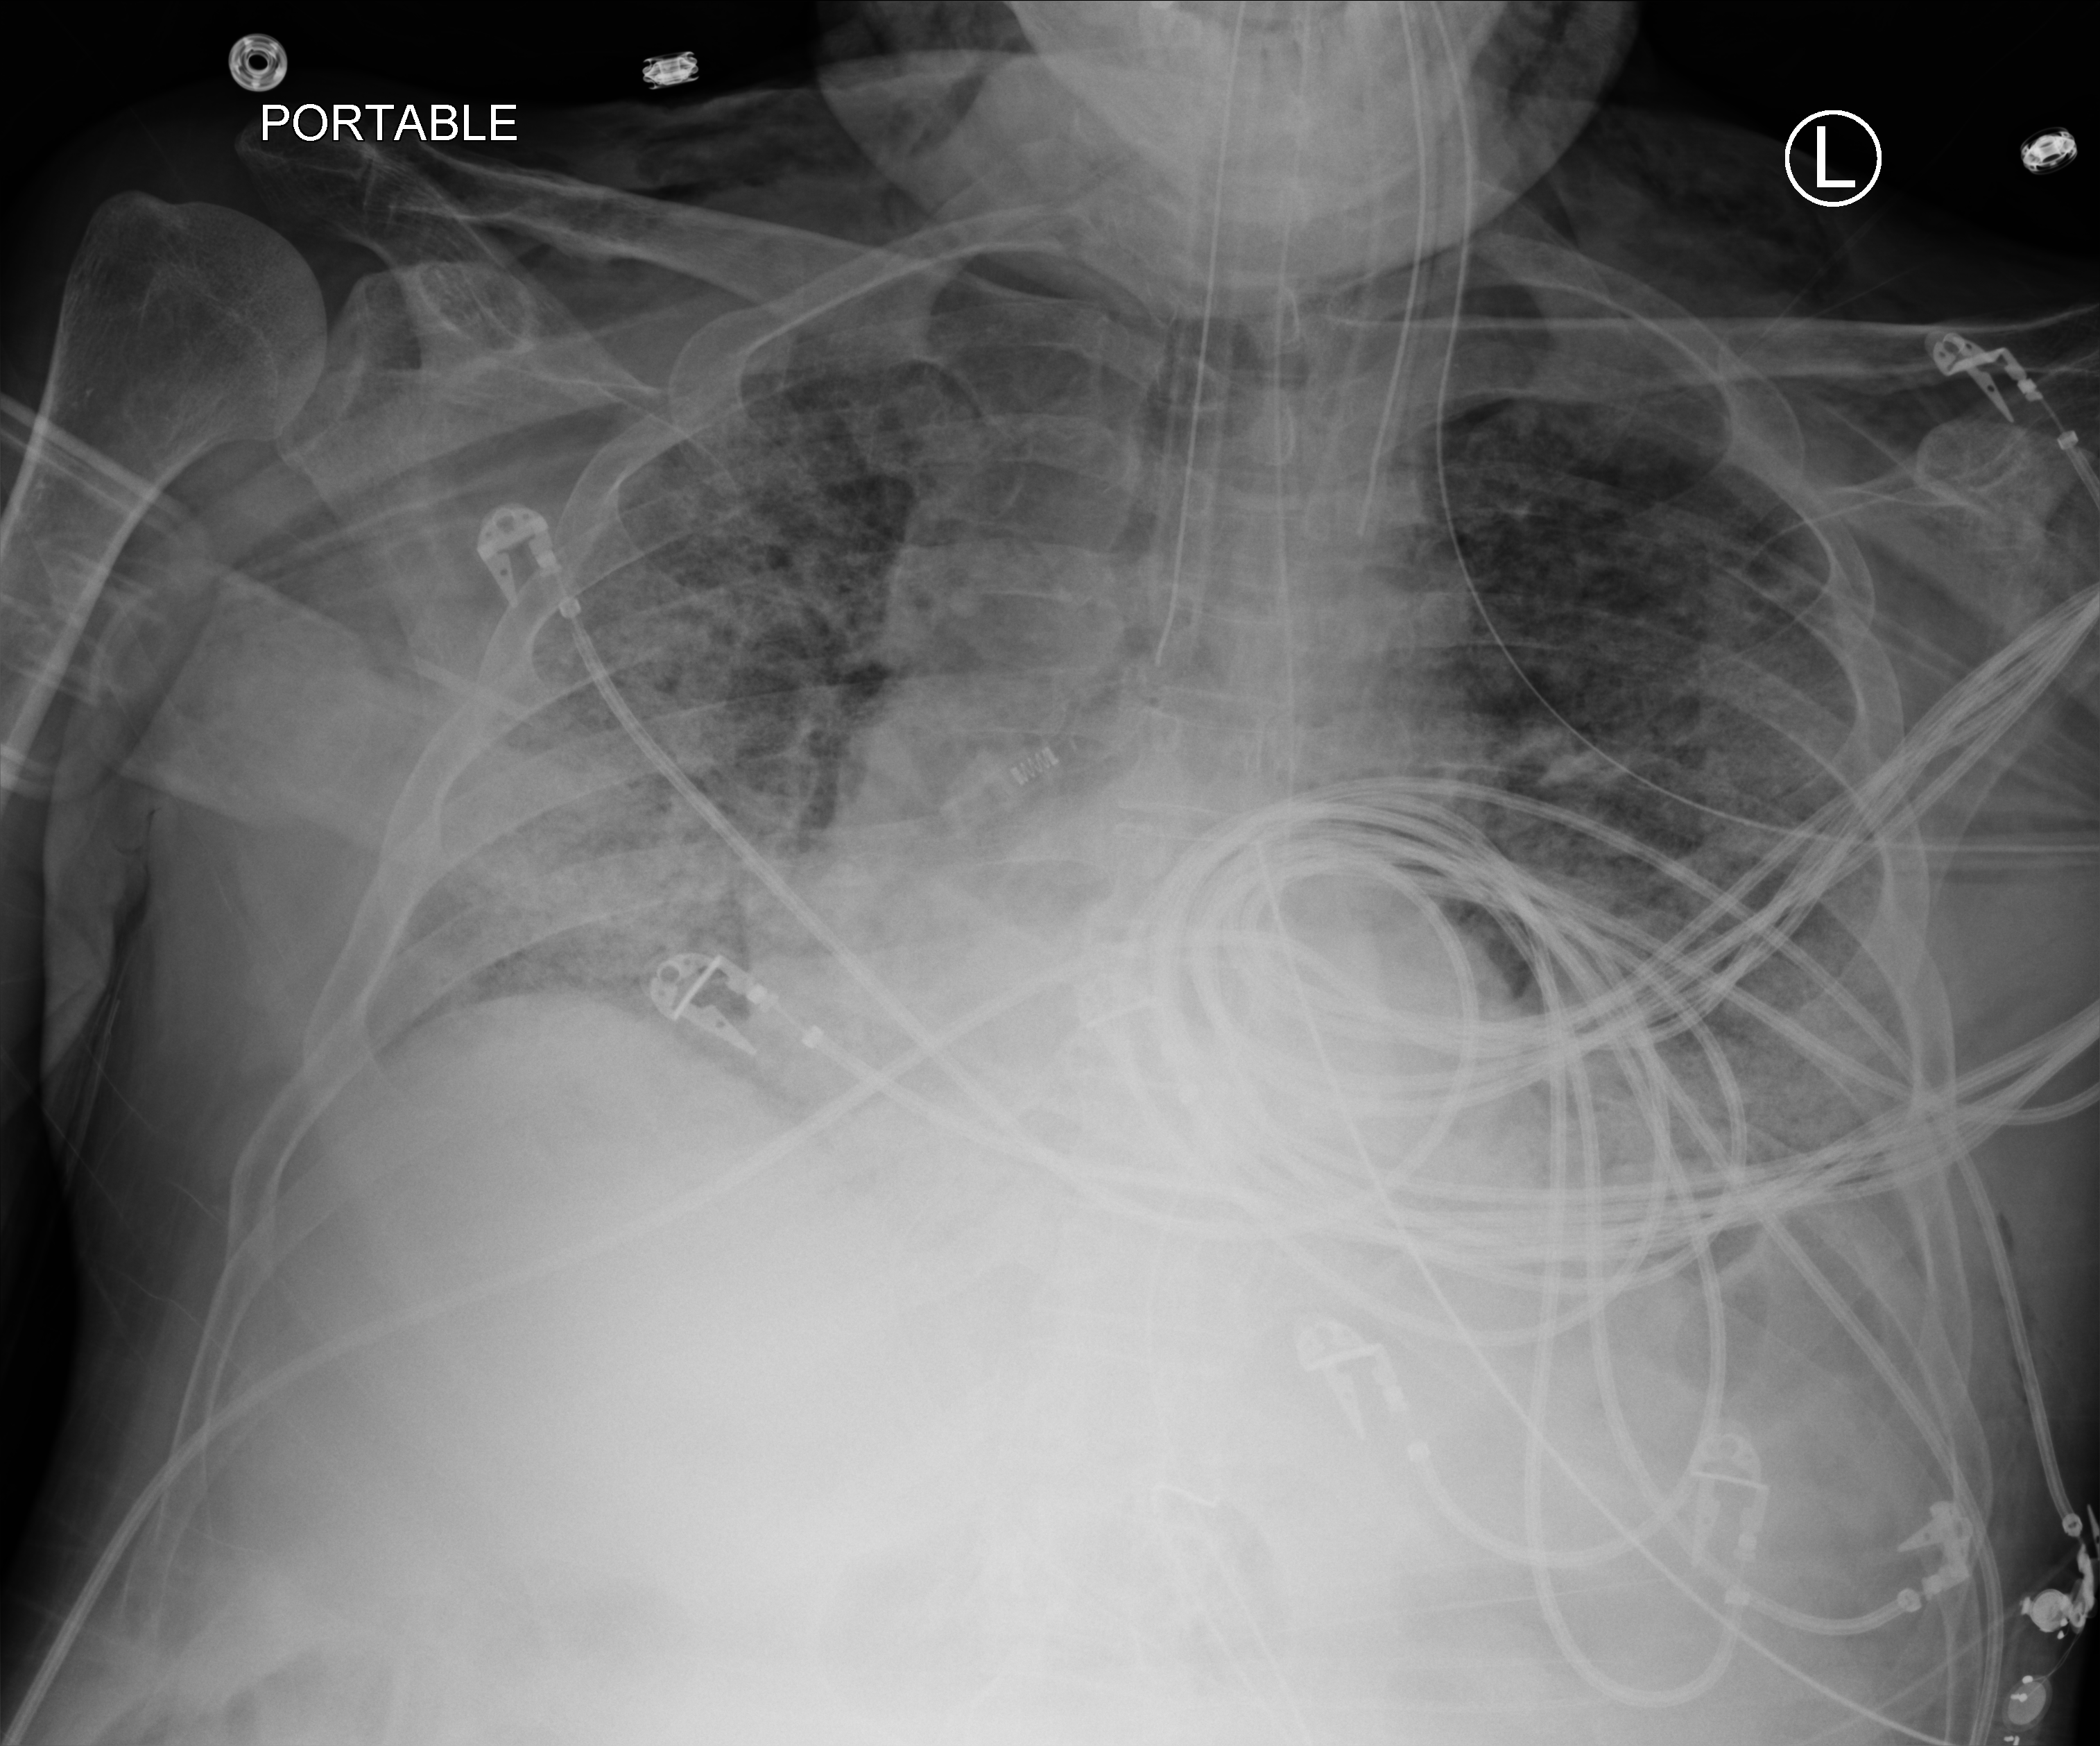
Portable chest radiograph; anteroposterior (AP) projection. Patient hospitalised with COVID-19; male, aged 60–74 years.
From the hospital-stay record, not from the radiograph (when in the stay this image was taken is not recorded): length of hospital stay: 54 days; mechanically ventilated during this hospital stay: yes; admitted to intensive care during this hospital stay: yes.